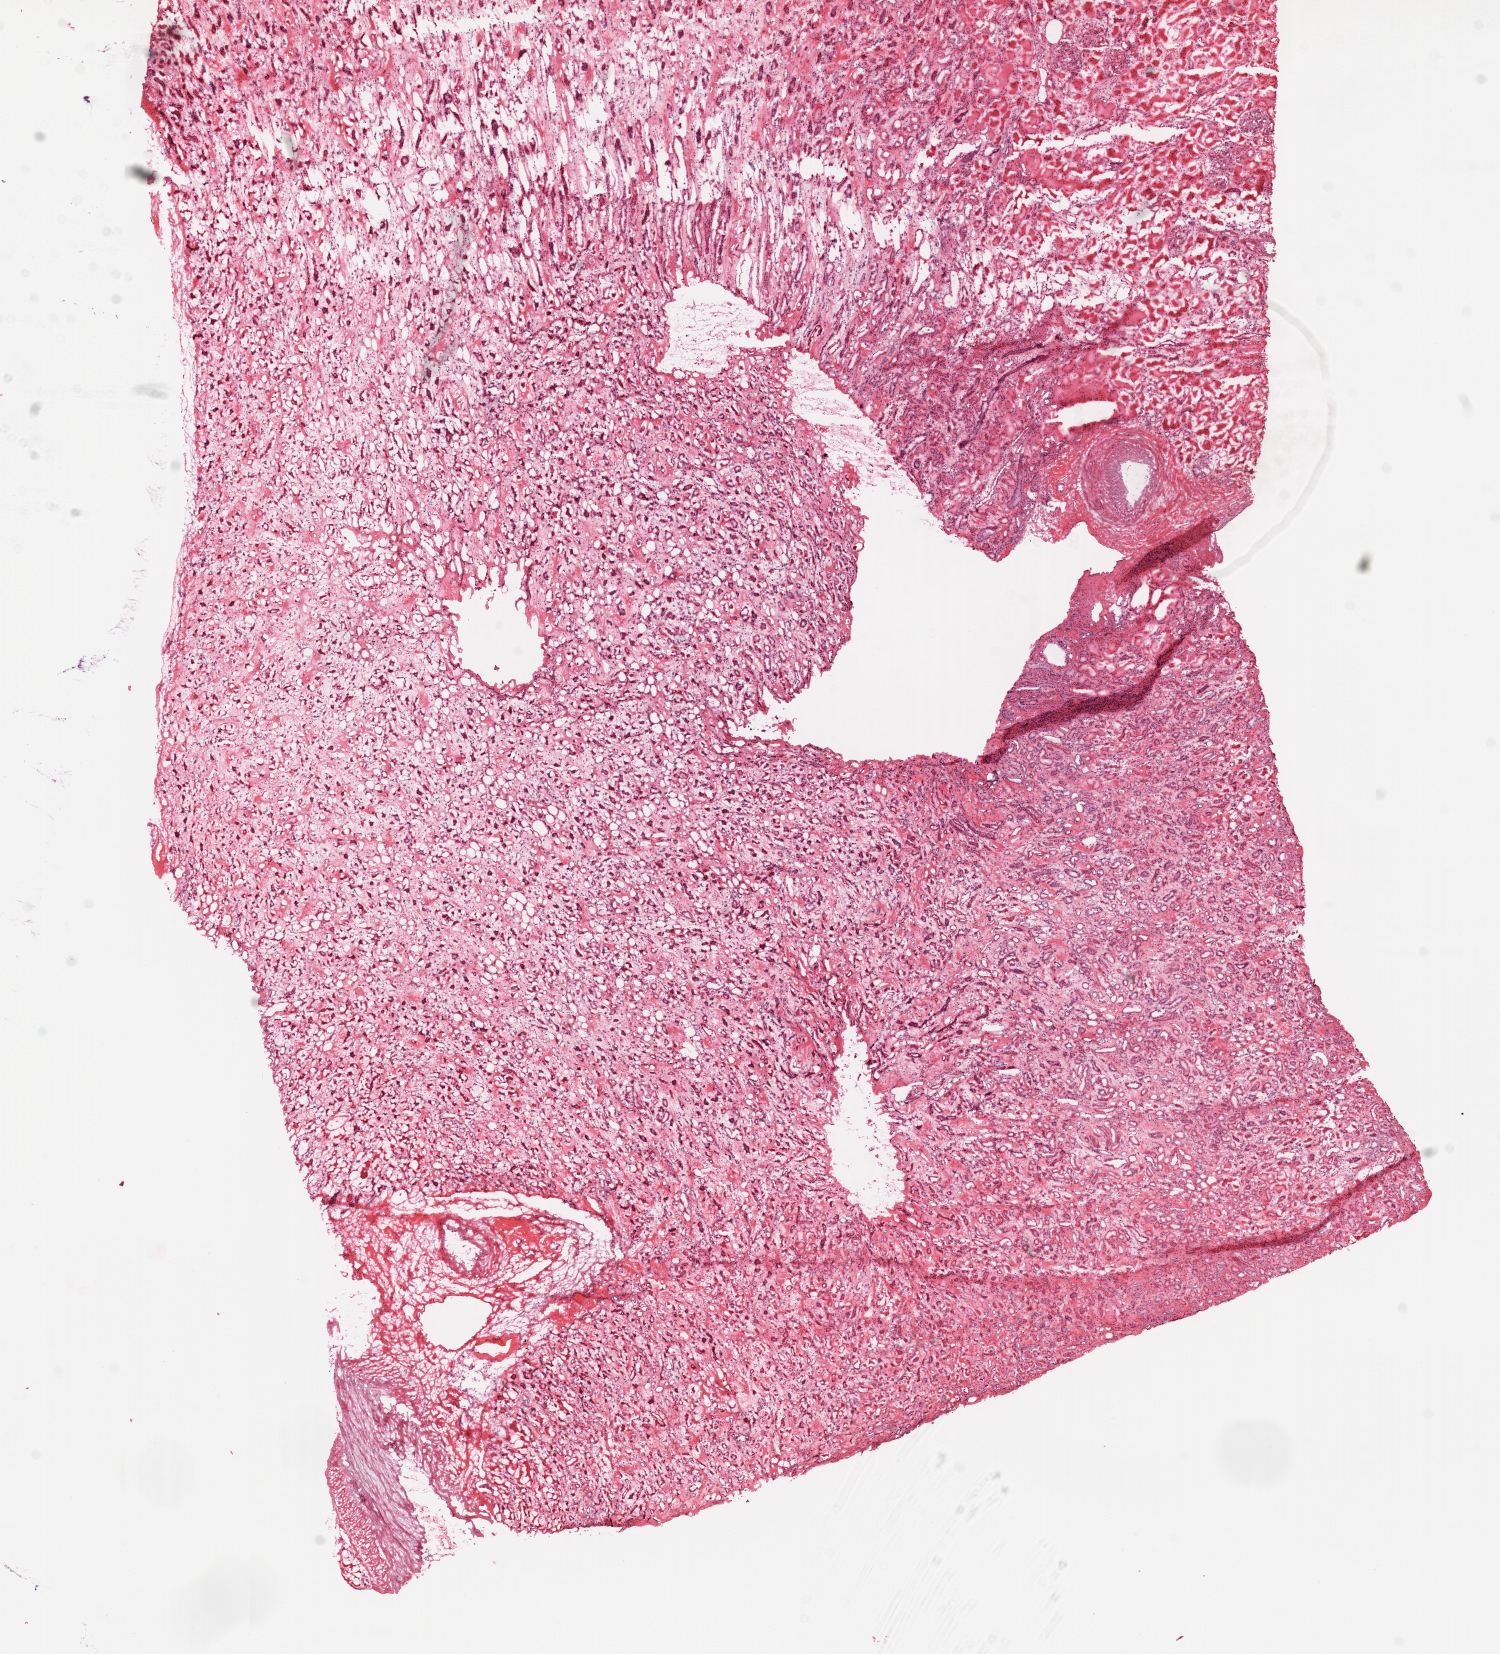
Hematoxylin and eosin (H&E) stained whole-slide image — a low-resolution overview of the entire scanned area, about 12.0 x 13.3 mm (from a 20x scan). Frozen section. Solid tissue normal (non-tumour tissue) sample from the kidney. Male patient; age at initial diagnosis 76 years.
* this section: solid tissue normal sample (biorepository sample class)
* patient diagnosis: Clear cell adenocarcinoma, NOS